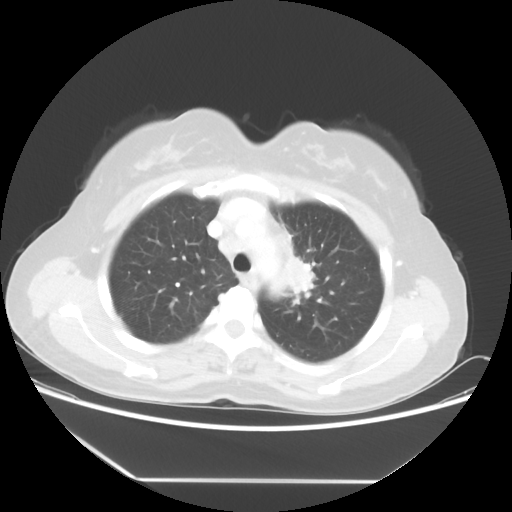
Chest CT, one axial slice; slice 40 of 52 in the series (ordered by position); reconstruction kernel STANDARD; lung window (W 1500 / L -600 HU); 5 mm slice thickness; 512 × 512 image matrix, field of view 390 × 390 mm. Patient: female, 50 years. Case-level facts recorded for this patient, not image findings: clinical TNM (as recorded): T2 N3 M0.
Outlined on this slice (bounding box drawn by a radiologist):
- lung tumour (recorded histology: adenocarcinoma): bounding box [x1, y1, x2, y2] px = [275, 248, 323, 303]